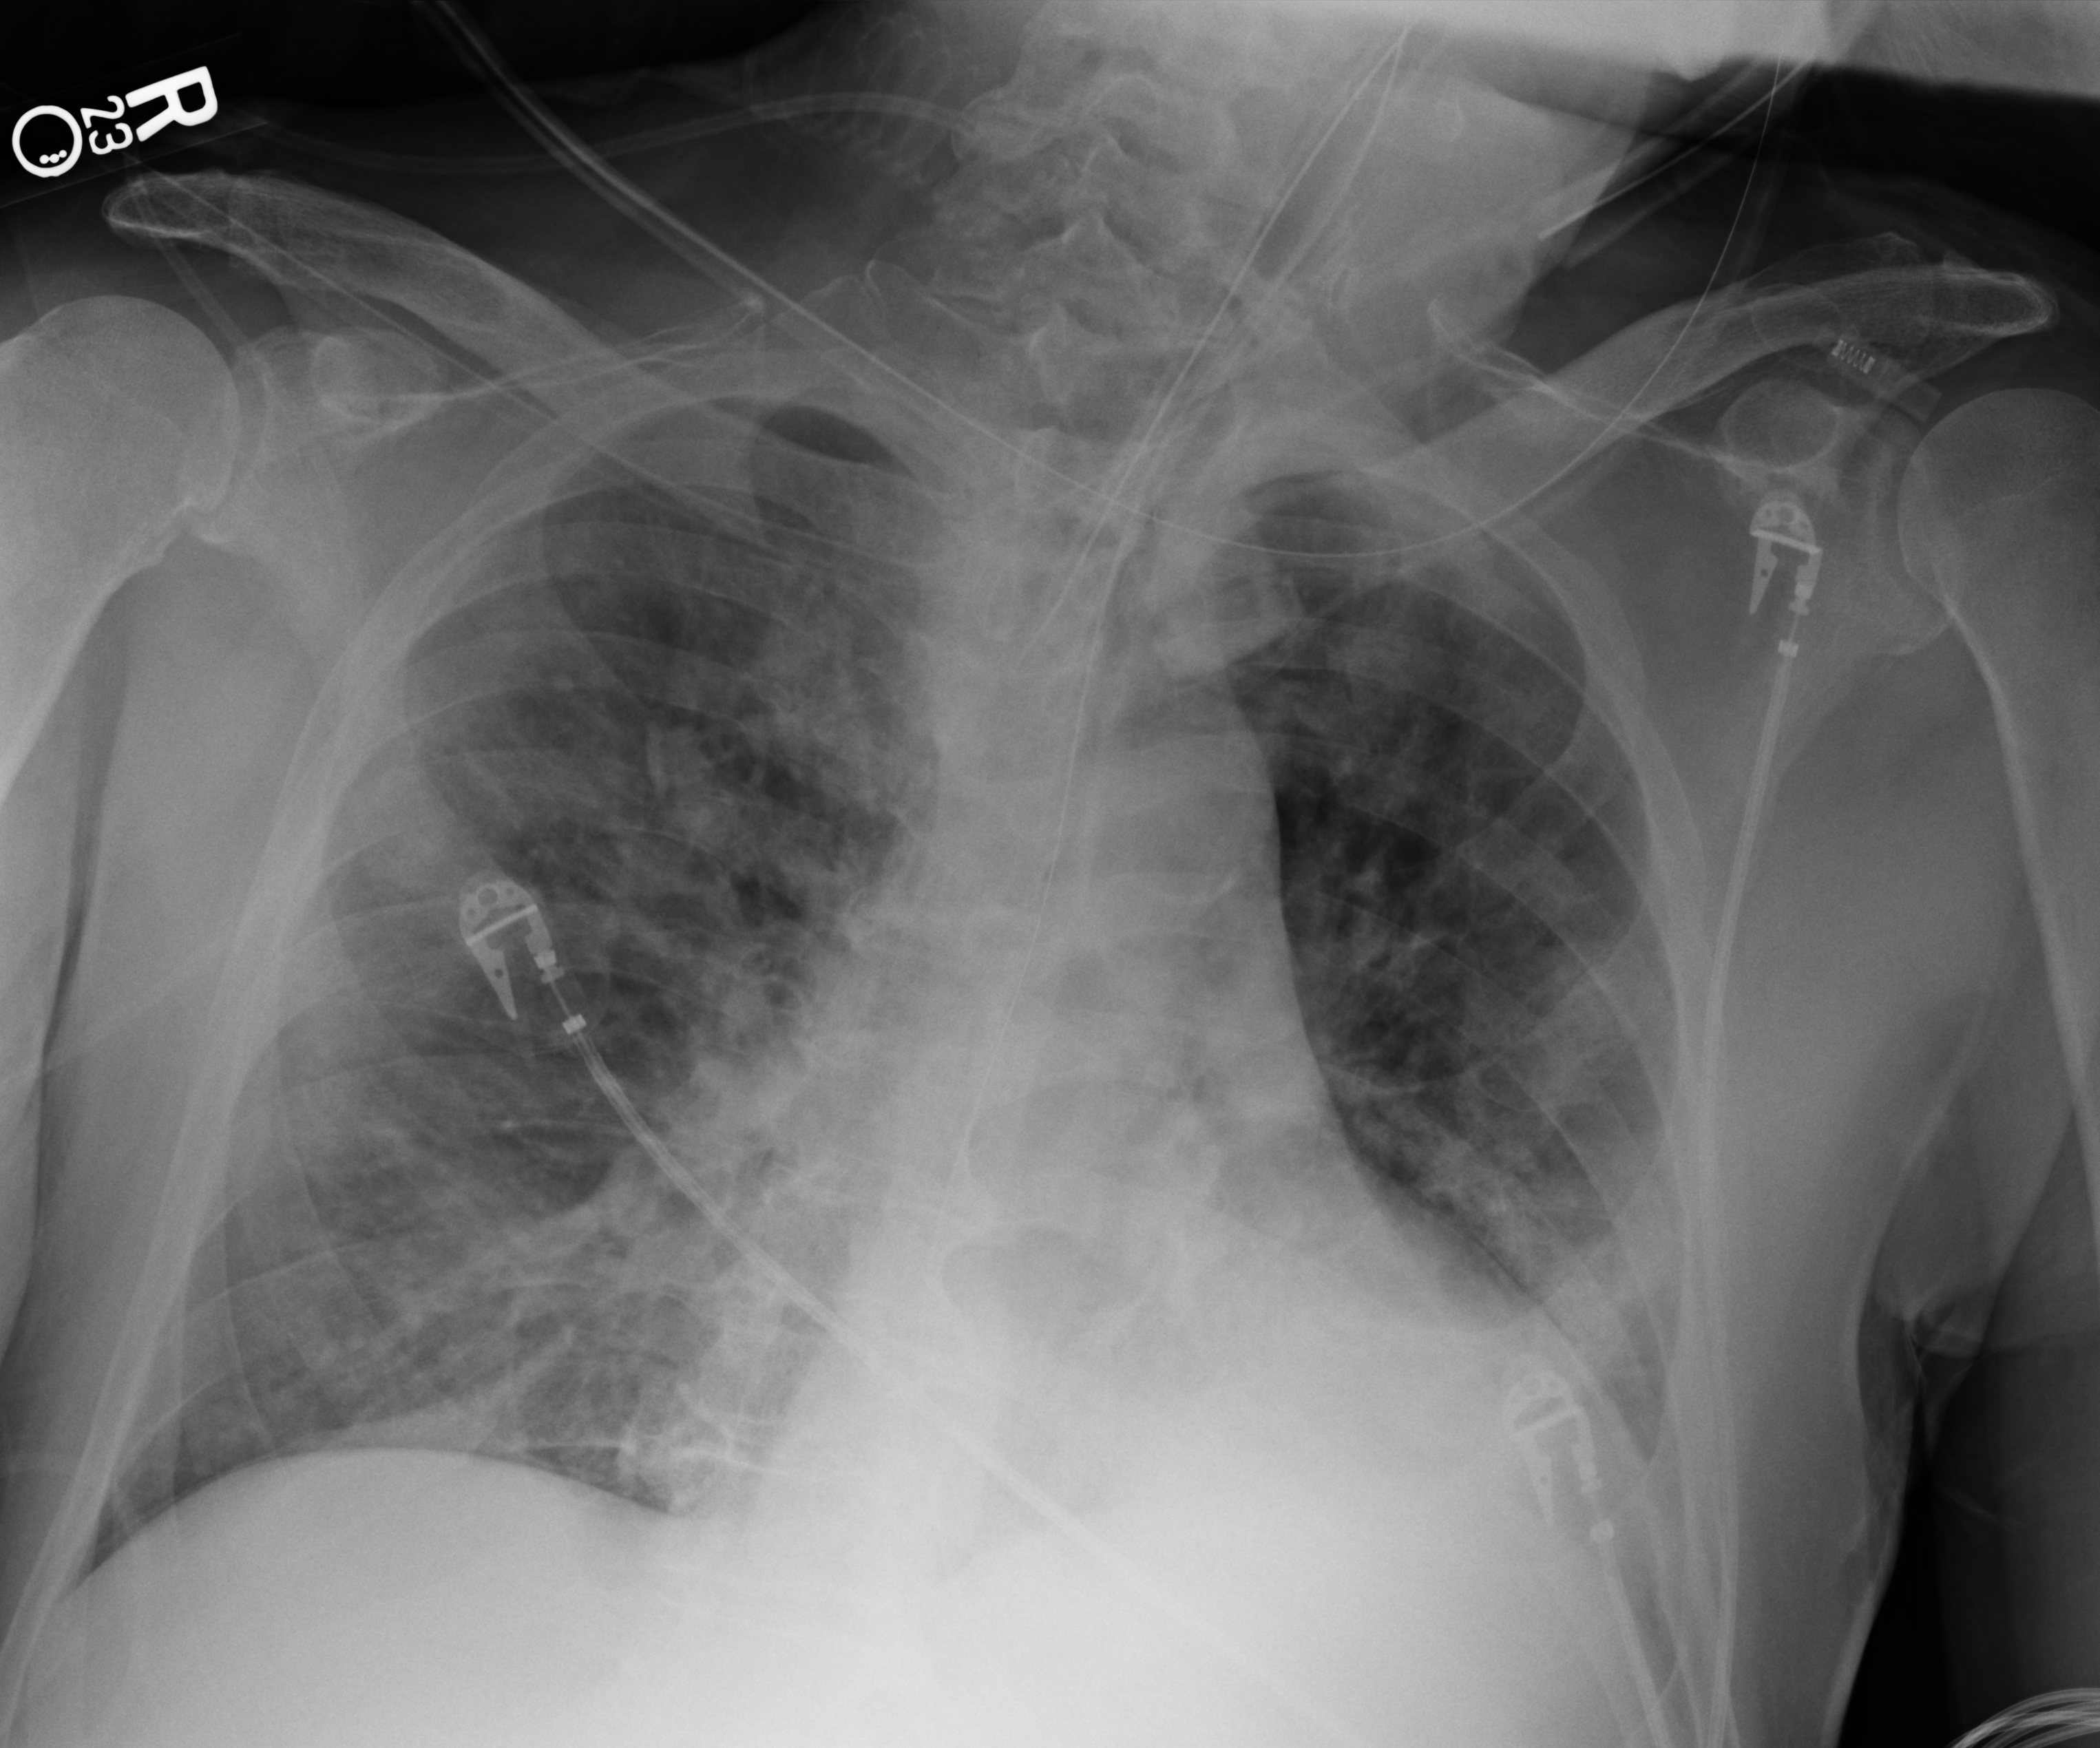
Chest X-ray (portable), anteroposterior (AP) projection. Male patient hospitalised with COVID-19, age 60–74 years.
Hospital-stay facts (about this admission, not read from this image; timing relative to this image not recorded):
- admitted to intensive care during this hospital stay: yes
- length of hospital stay: 35 days
- mechanically ventilated during this hospital stay: yes